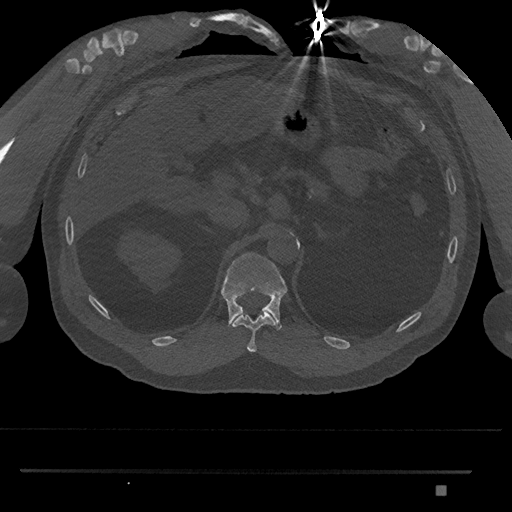
CT including the spine, one axial slice. Position 915 of 1134 along the scan axis. Reconstruction kernel Br40s/3. 120 kVp. Bone window (W 1800 / L 400 HU). 0.5 mm slice thickness. 512 × 512 image matrix, field of view 429 × 429 mm. Patient: male, 65 years. Case-level facts recorded for this patient, not image findings: primary cancer: prostate.
Annotated regions visible in this slice (semi-automatic segmentation, software-assisted and operator-edited):
- T11 vertebra: box from (x=232, y=312) to (x=275, y=352) px
- T12 vertebra: (x=221, y=252)–(x=288, y=330)